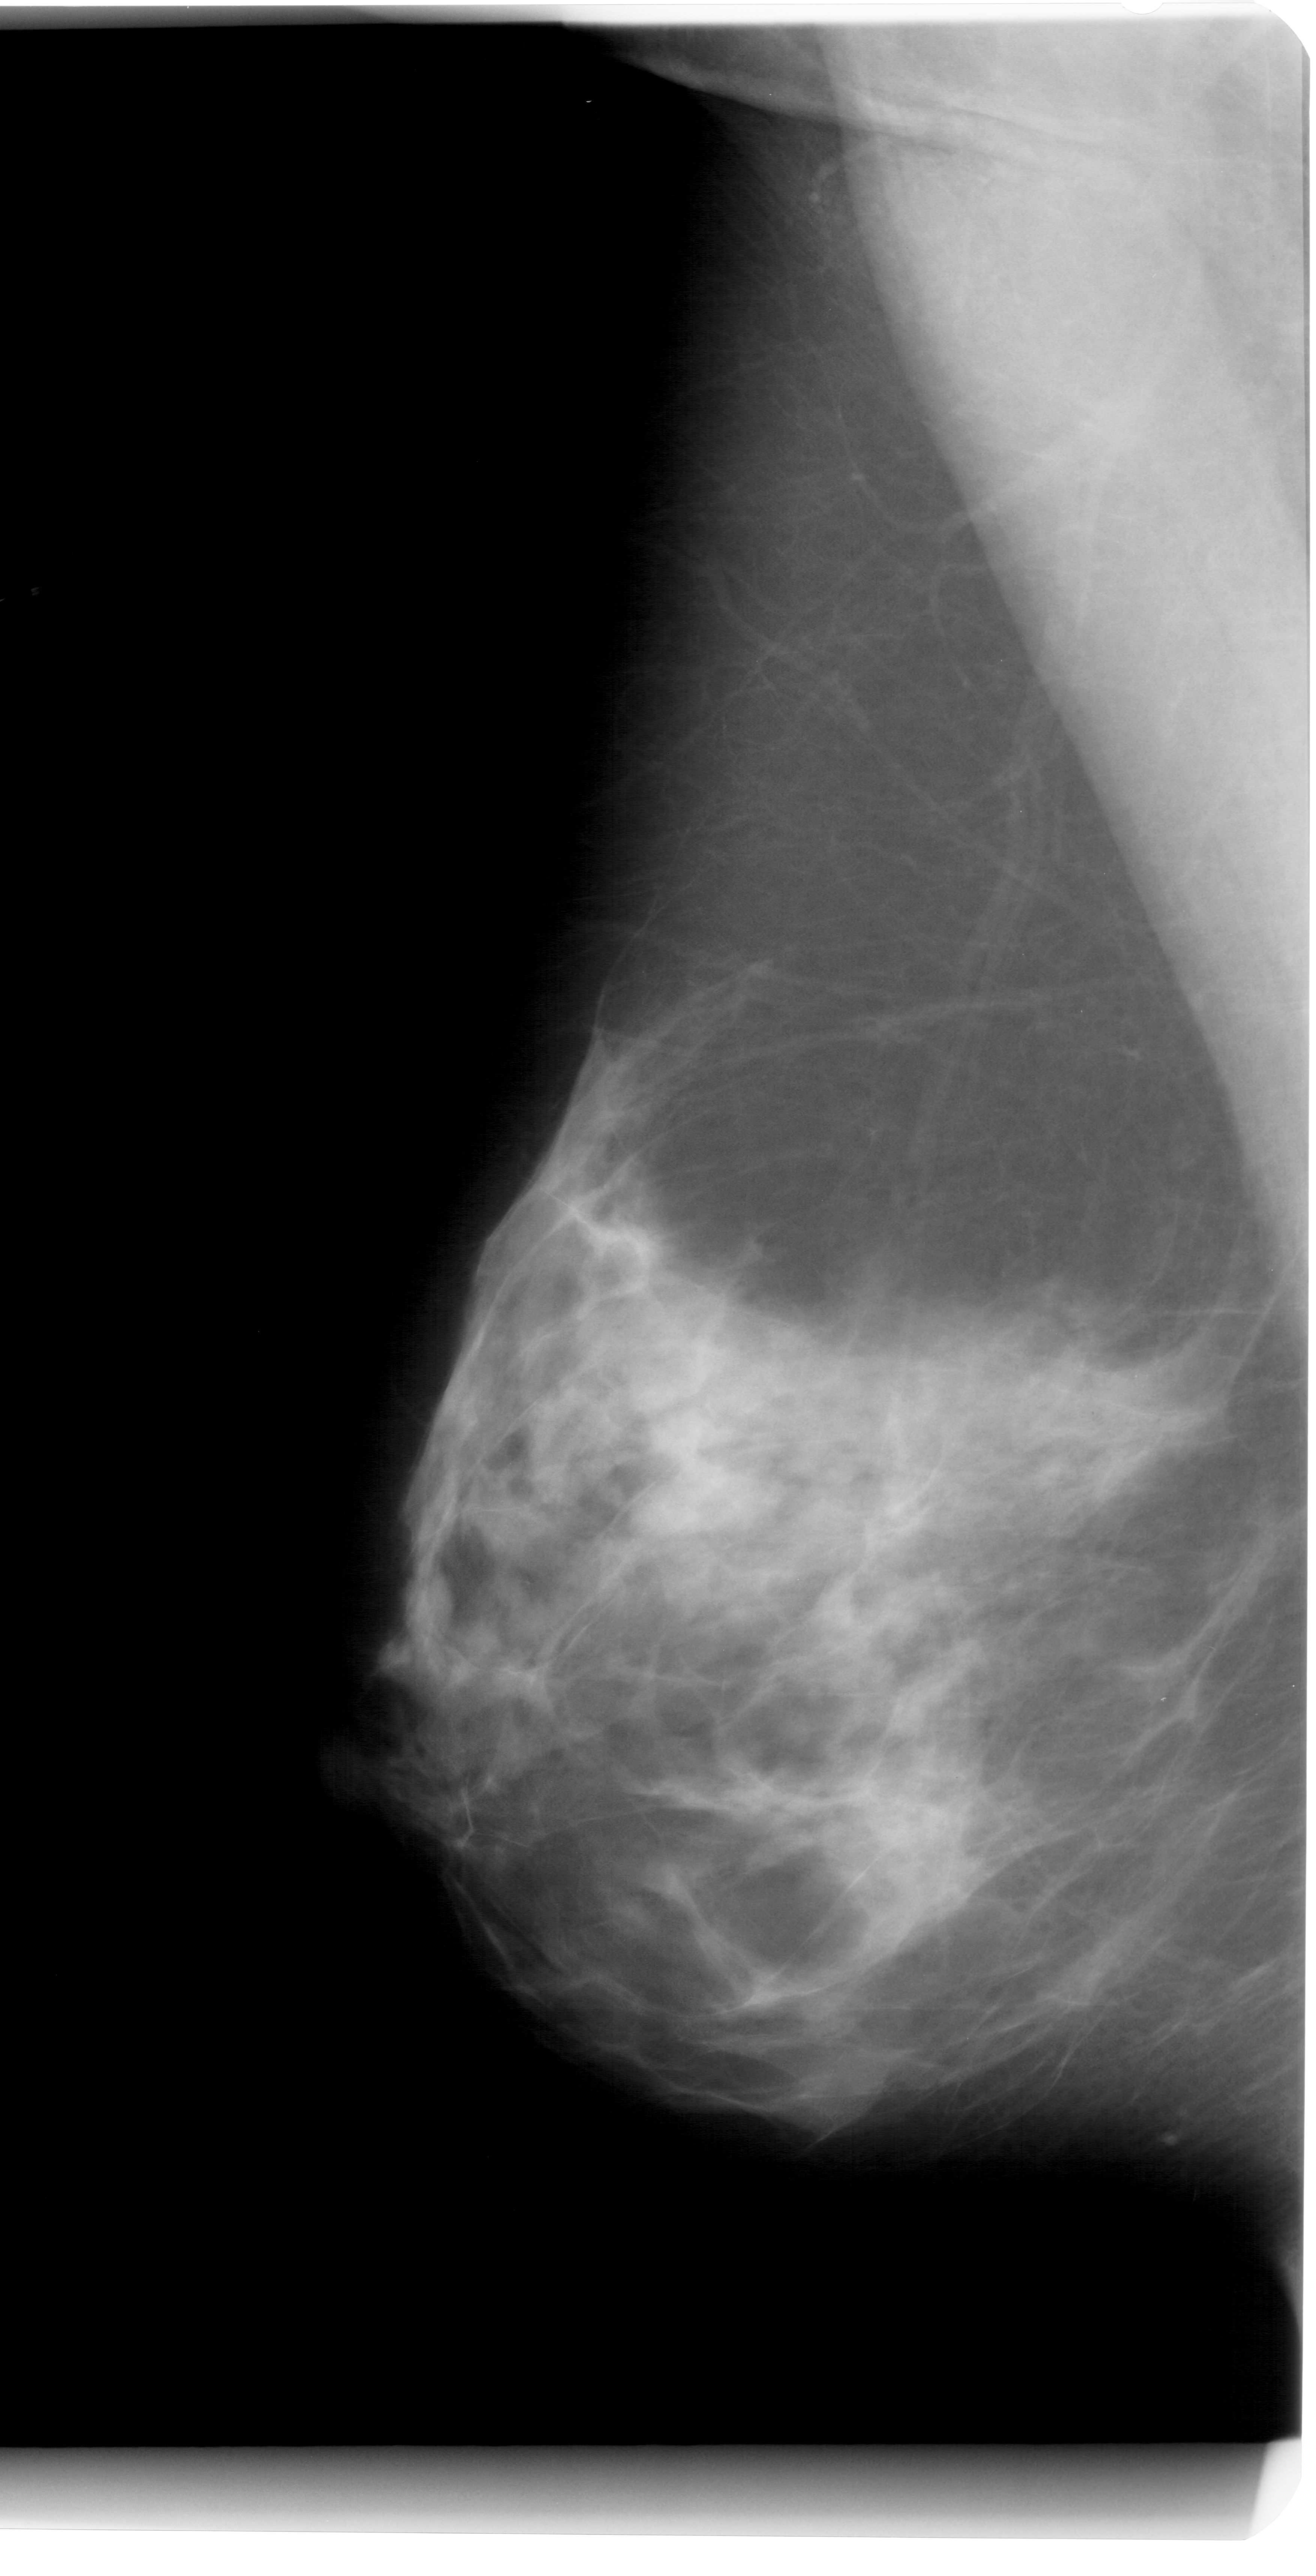
Digitized screen-film mammogram; left breast; MLO view; BI-RADS breast density category 4 (scale 1–4); 1316 × 2576 image matrix.
Expert-marked regions of interest on this film, with their recorded descriptors:
- mass, shape irregular, margins ill defined; BI-RADS assessment category 4; pathology result (as recorded, not read from the image): benign: bounding box (x1, y1, x2, y2) in pixels: (547, 1149, 687, 1286)